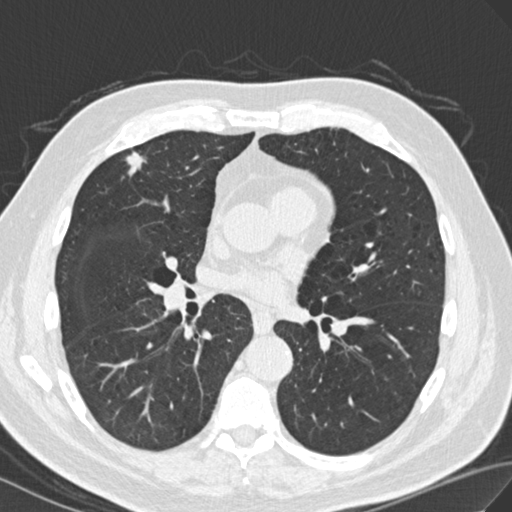
Low-dose screening chest CT, one axial slice; reconstruction kernel B30f; 120 kVp; lung window (W 1500 / L -600 HU); 512 × 512 image matrix.
Annotated regions visible in this slice (outlined manually by an expert reader):
- lesion 1 (tumor, upper lobe of right lung): bounding box (x1, y1, x2, y2) in pixels: (126, 152, 146, 175)